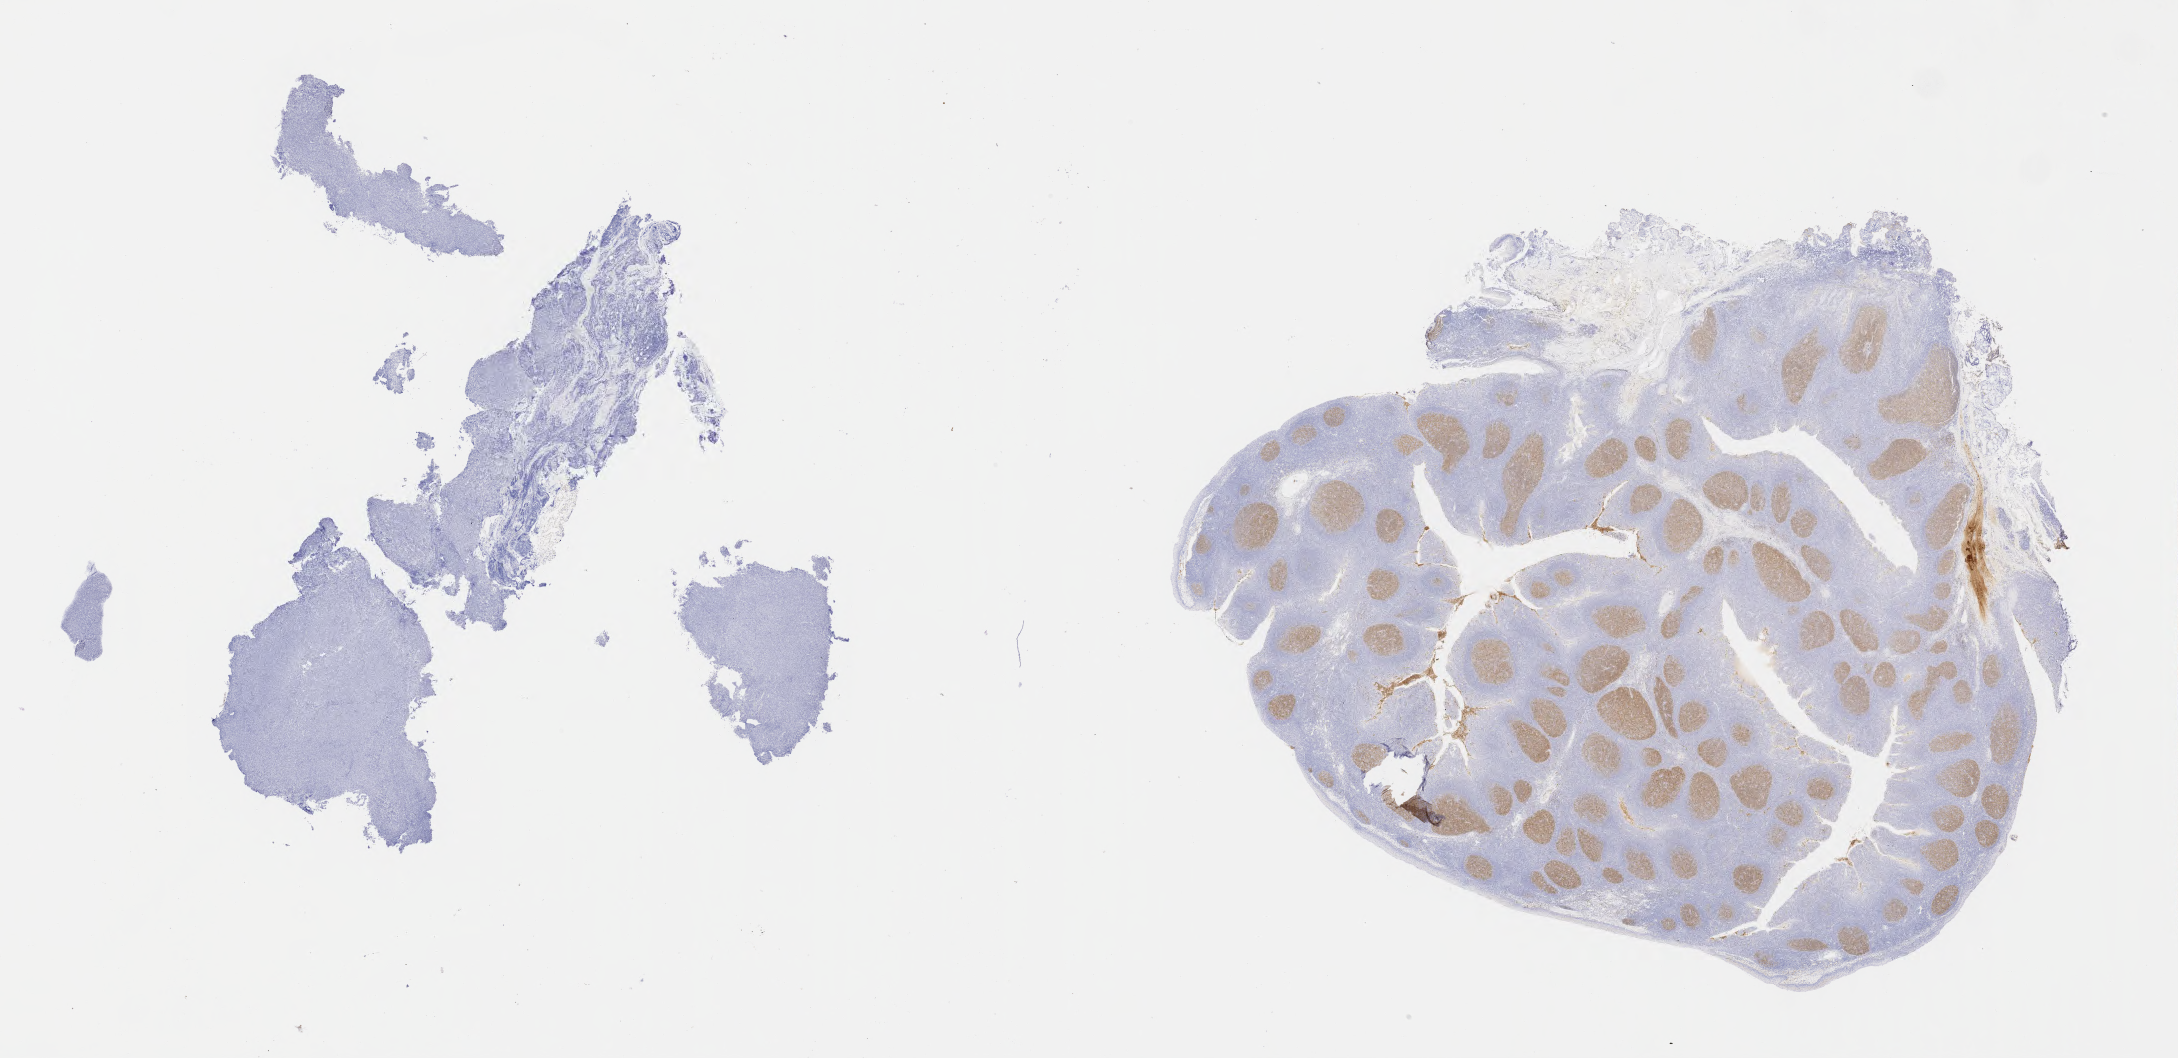
Whole-slide image, immunohistochemical stain for CD10 — a low-resolution overview of the entire scanned area, about 35.2 x 17.1 mm; tumor tissue; site: liver. Patient: female, age 36 years.
Diagnosis: Diffuse large B-cell lymphoma, NOS.